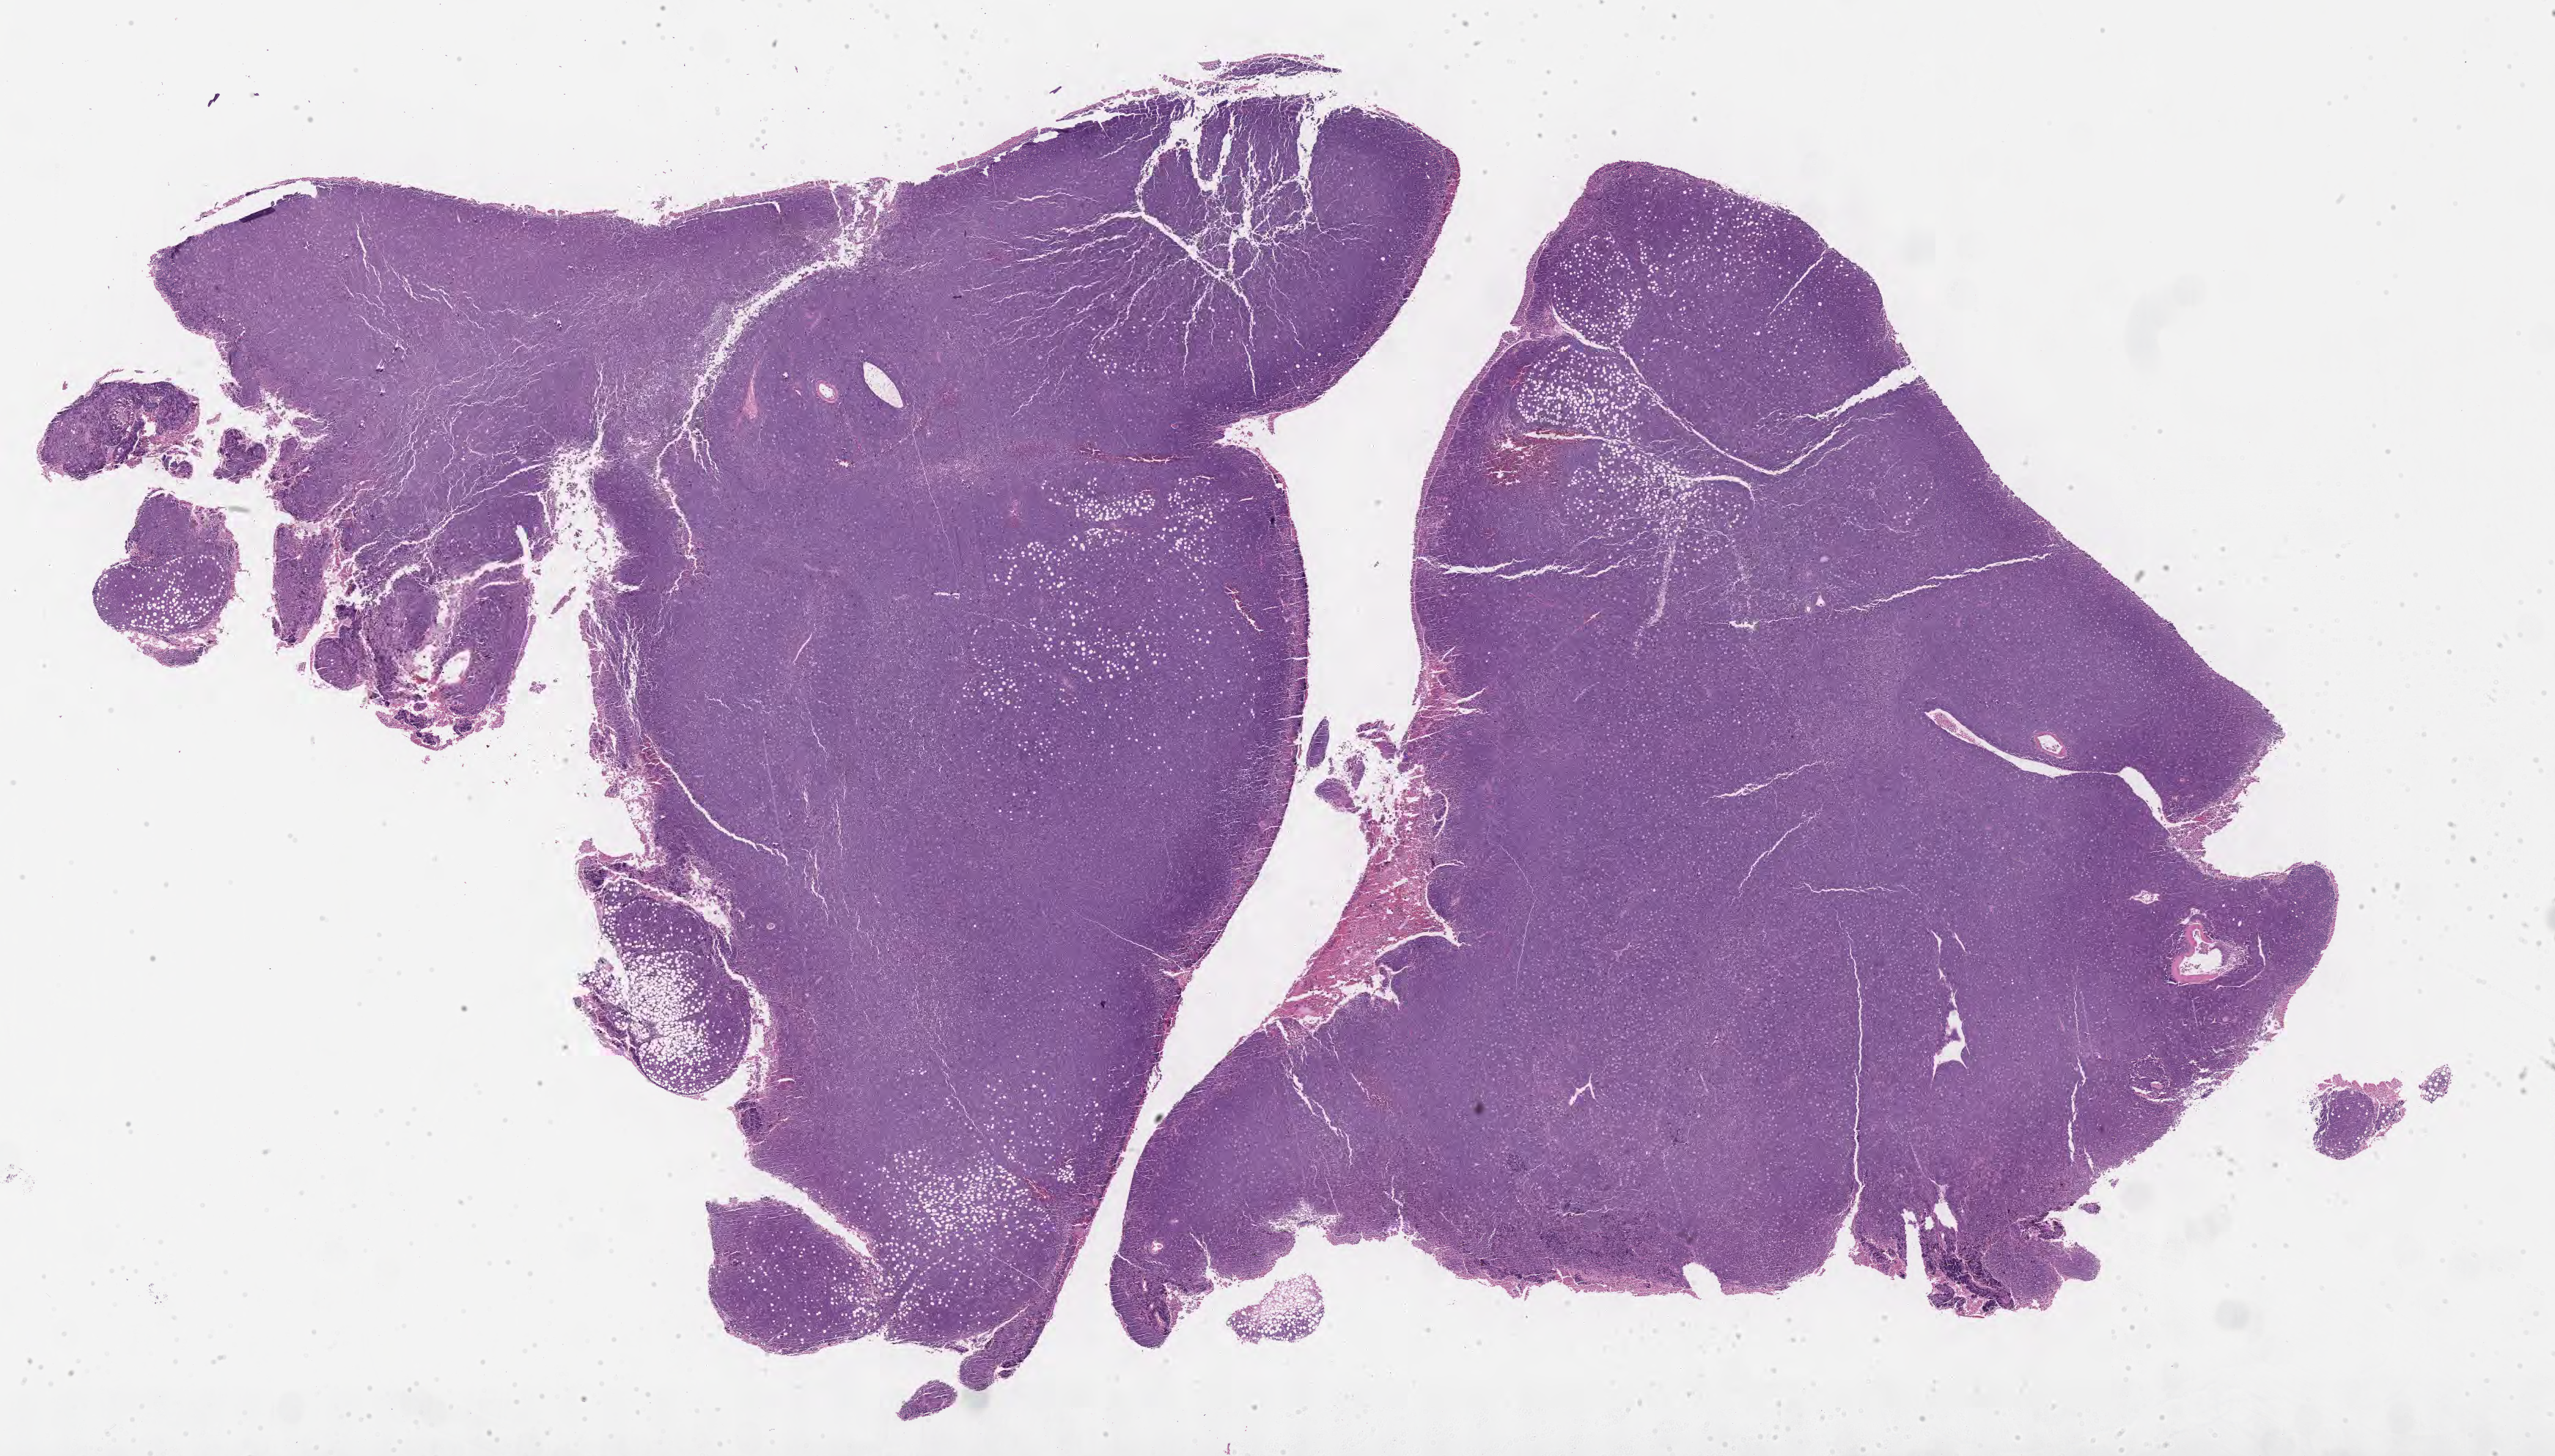
Whole-slide image, H&E stain, whole scanned area (about 28.2 x 16.1 mm) shown as a low-resolution overview. Specimen: tumor tissue. Site: peritoneum. Patient: male, age at initial diagnosis 9 years.
• diagnosis: Burkitt lymphoma, NOS